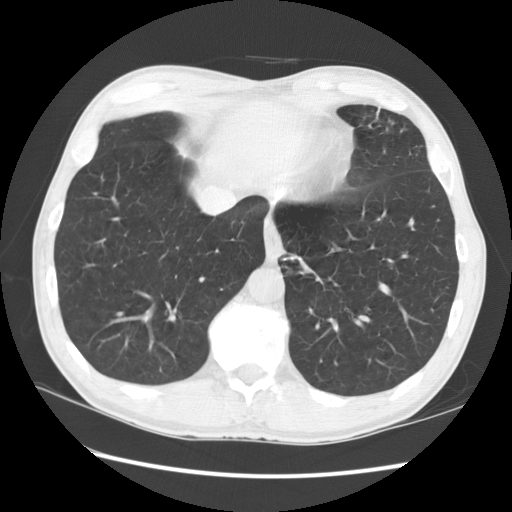
Low-dose screening chest CT, one axial slice; position 33 of 141 along the scan axis; reconstruction kernel STANDARD; lung window (W 1500 / L -600 HU); 512 × 512 image matrix, field of view 360 × 360 mm.
Annotated regions visible in this slice (expert manual segmentation):
- lesion 1 (tumor, lower lobe of left lung): bounding box (x1, y1, x2, y2) in pixels: (376, 111, 378, 119)